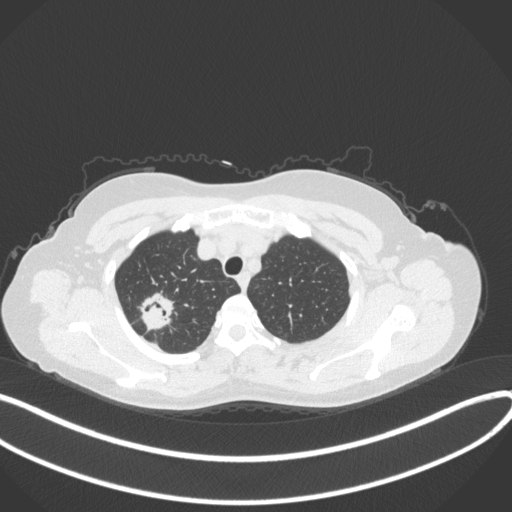
Chest CT, one axial slice; position 304 of 342 along the scan axis; reconstruction kernel B31f; 120 kVp; lung window (W 1500 / L -600 HU); 512 × 512 image matrix. Female patient, age 50 years. Case-level facts recorded for this patient, not image findings: clinical TNM (as recorded): T1c N0 M0.
Annotated regions visible in this slice (bounding box drawn by a radiologist):
- lung tumour (recorded histology: adenocarcinoma): box from (x=137, y=292) to (x=175, y=332) px